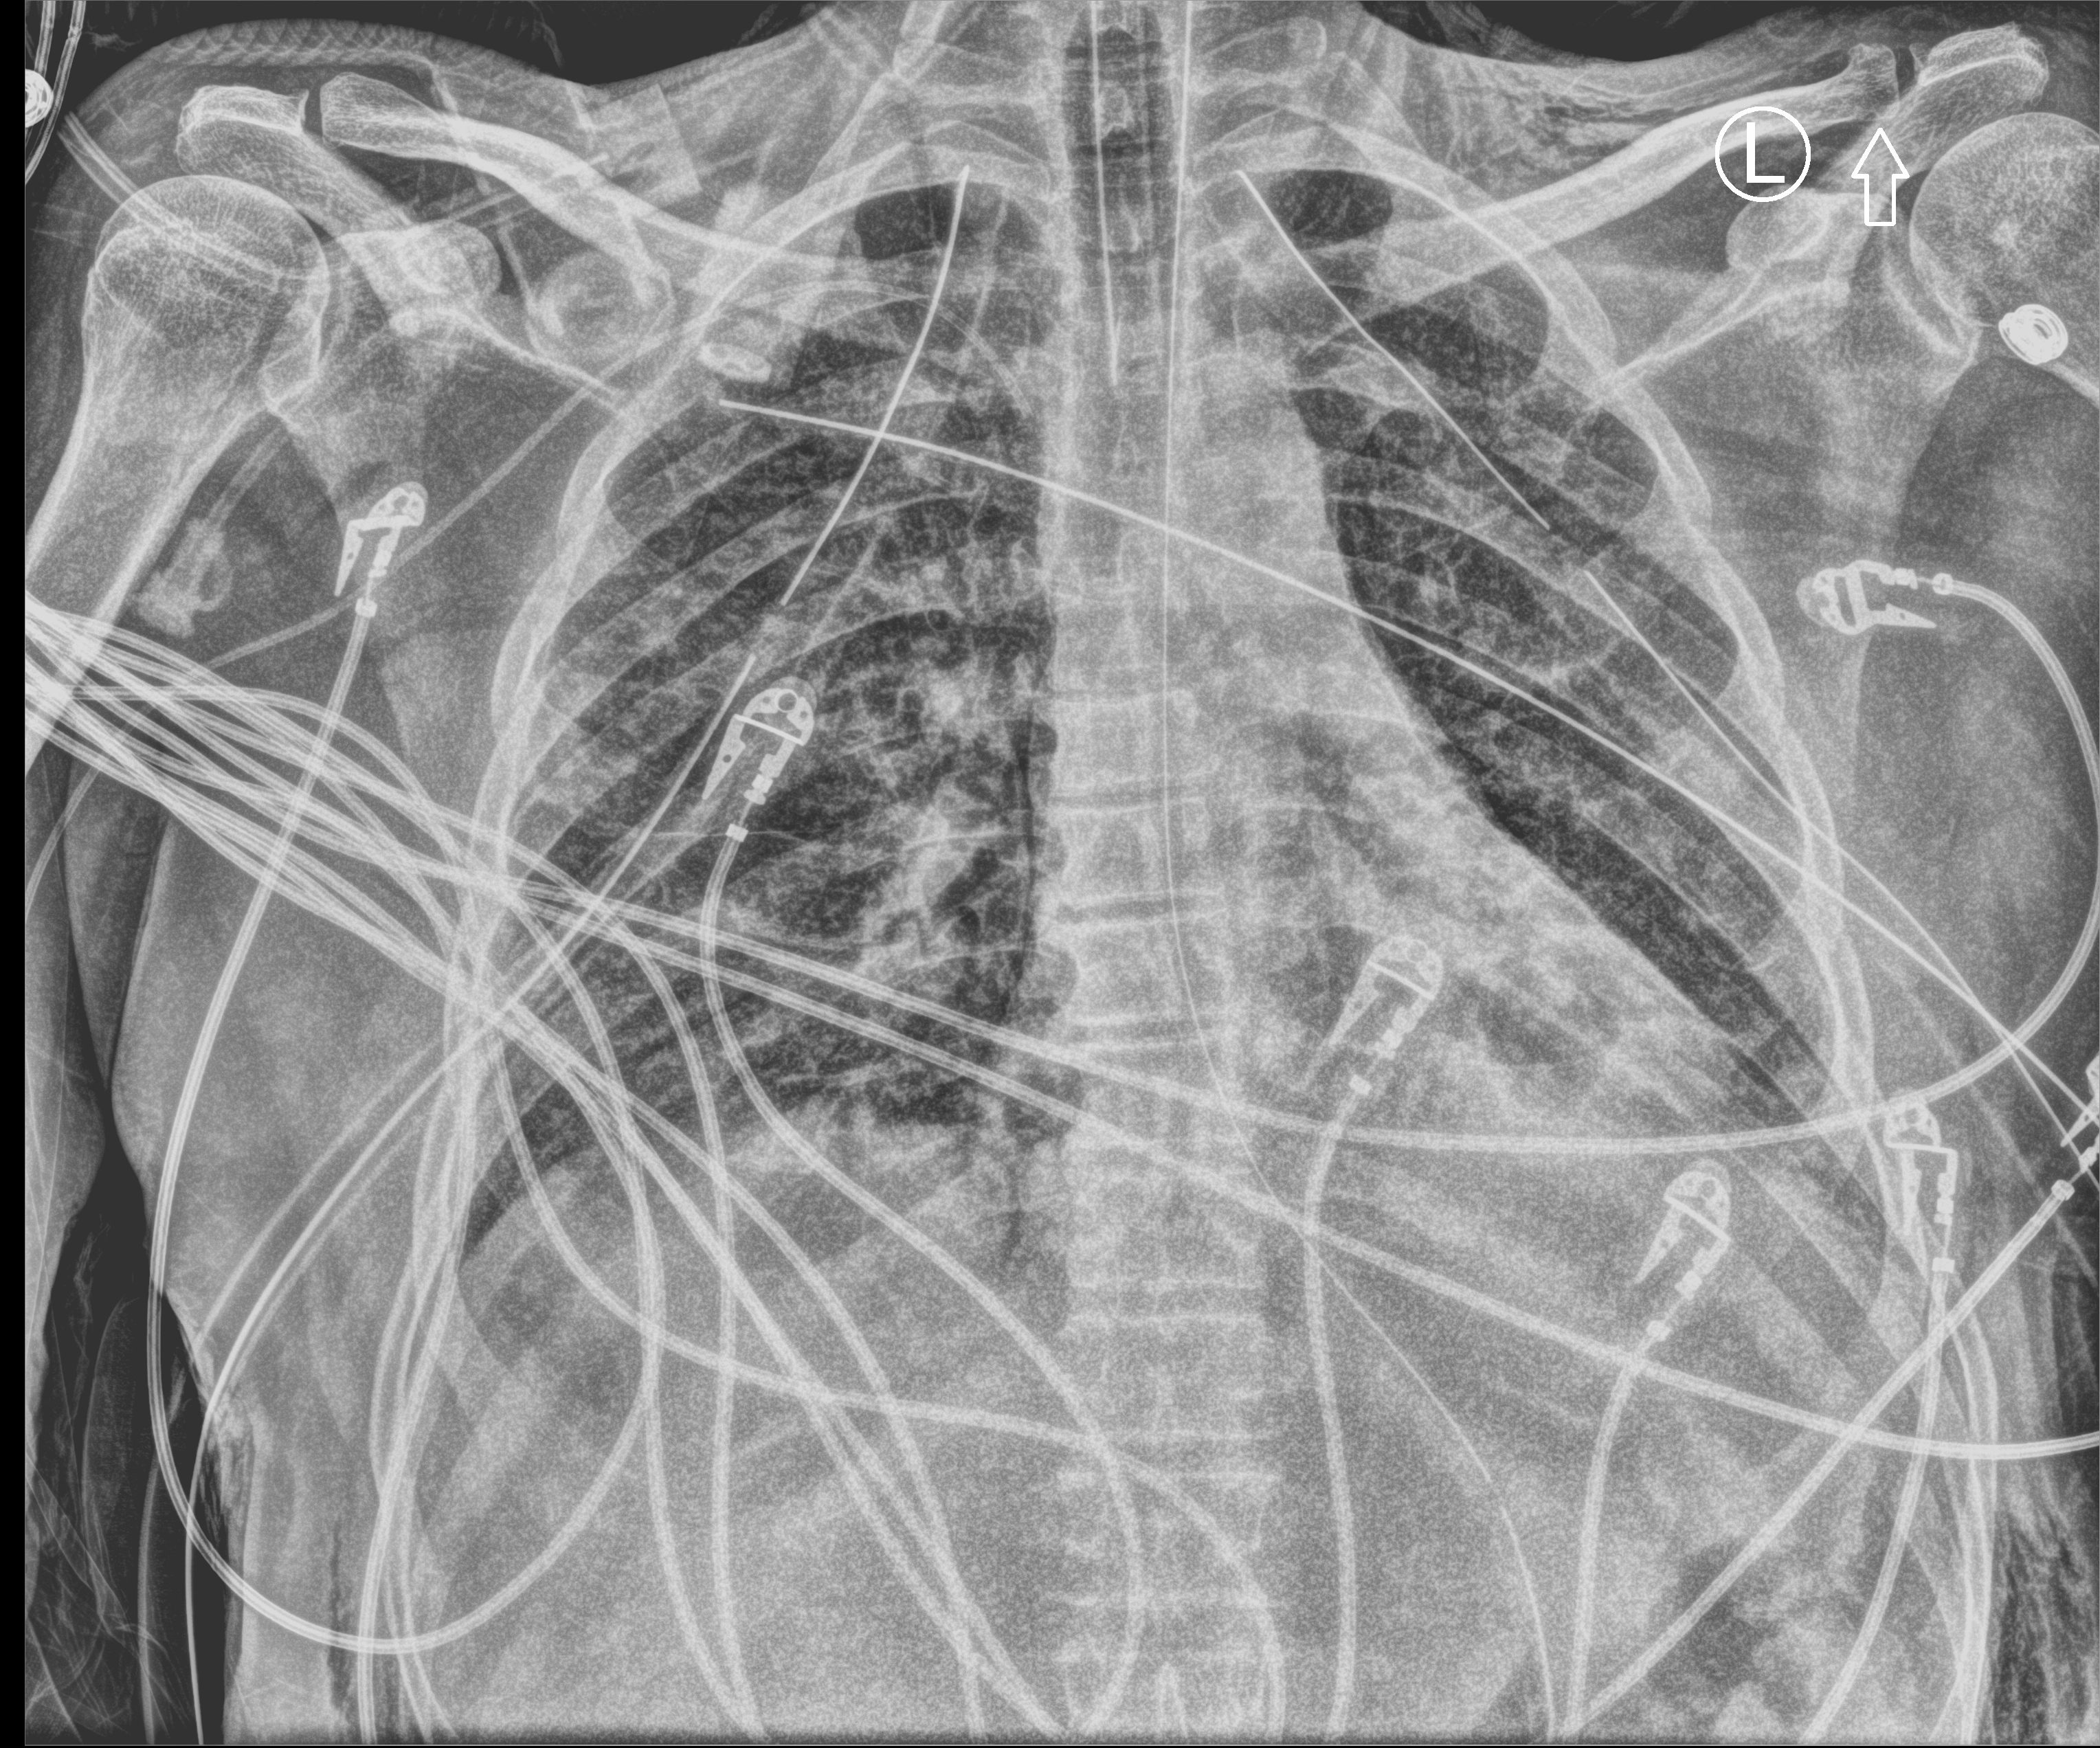
Chest X-ray (portable); anteroposterior (AP) projection. Male patient hospitalised with COVID-19, age 18–59 years.
Hospital-stay facts (about this admission, not read from this image; timing relative to this image not recorded): admitted to intensive care during this hospital stay: yes.